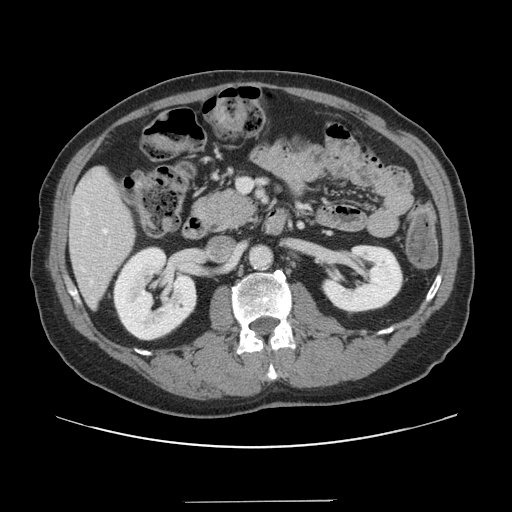
Contrast-enhanced abdominal CT, one axial slice. Slice 58 of 151 in the series (ordered by position). 120 kVp. Intravenous contrast given. Soft-tissue window (W 400 / L 40 HU). 2.5 mm slice thickness. 512 × 512 image matrix, field of view 399 × 399 mm. Male patient, age 63 years. Case-level facts recorded for this patient, not image findings: diagnosis: colorectal cancer liver metastases, imaged before liver resection; multiple liver metastases: no.
Outlined on this slice (outlined manually by an expert reader):
- hepatic veins: bounding box (x1, y1, x2, y2) in pixels: (103, 229, 107, 233)
- liver: (70, 169, 135, 304)
- planned liver remnant (the part of the liver to remain after resection): (70, 169, 135, 304)
- portal vein (with intrahepatic branches): (238, 179, 253, 193)